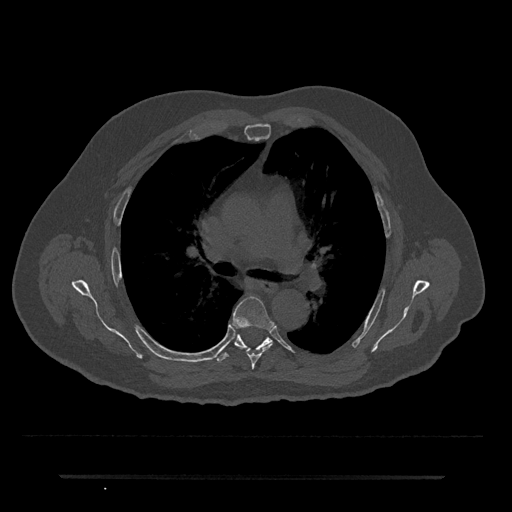
CT including the spine, one axial slice; slice 463 of 797 in the series (ordered by position); reconstruction kernel Br40s/3; 120 kVp; bone window (W 1800 / L 400 HU); 0.5 mm slice thickness; 512 × 512 image matrix, field of view 437 × 437 mm. Male patient, age 69 years. Case-level facts recorded for this patient, not image findings: primary cancer: prostate.
Outlined on this slice (semi-automatic segmentation, software-assisted and operator-edited):
- T5 vertebra: bounding box <233,296,274,369> (left, top, right, bottom; pixels)
- T6 vertebra: <217,334,272,362>